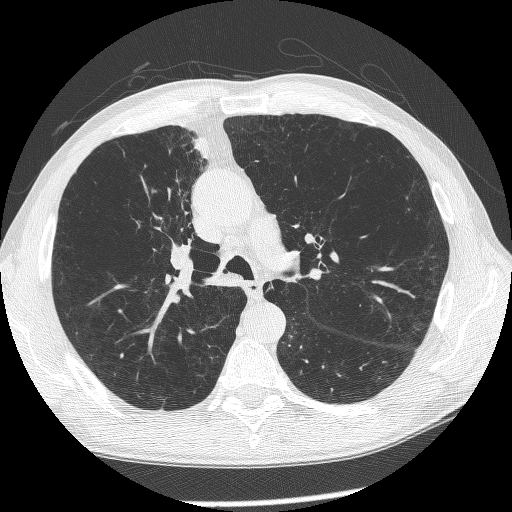
Chest CT (low-dose screening protocol), one axial image, first (baseline) screen, lung window (W 1500 / L -600 HU), 1.25 mm slice thickness, slice 162 of 266 in the series, 512 × 512 image matrix. Male, age 60 years at enrolment. Current smoker at enrolment.
• Lesion marked by an expert reader, box from (x=144, y=214) to (x=228, y=306) px.
• Reader record for this screening exam (exam-level; its link to the box is not recorded): non-calcified nodule or mass ≥4 mm, right upper lobe, 12 × 8 mm, spiculated (stellate) margins, mixed attenuation.
• Official screen result: positive, change unspecified: nodule(s) >= 4 mm or enlarging nodule(s), mass(es), or other non-specific abnormalities suspicious for lung cancer.
• Lung cancer was diagnosed 208 days after this screen: squamous cell carcinoma, NOS, right upper lobe, right middle lobe, right main stem bronchus, poorly differentiated (G3), stage IV (AJCC 6th edition).